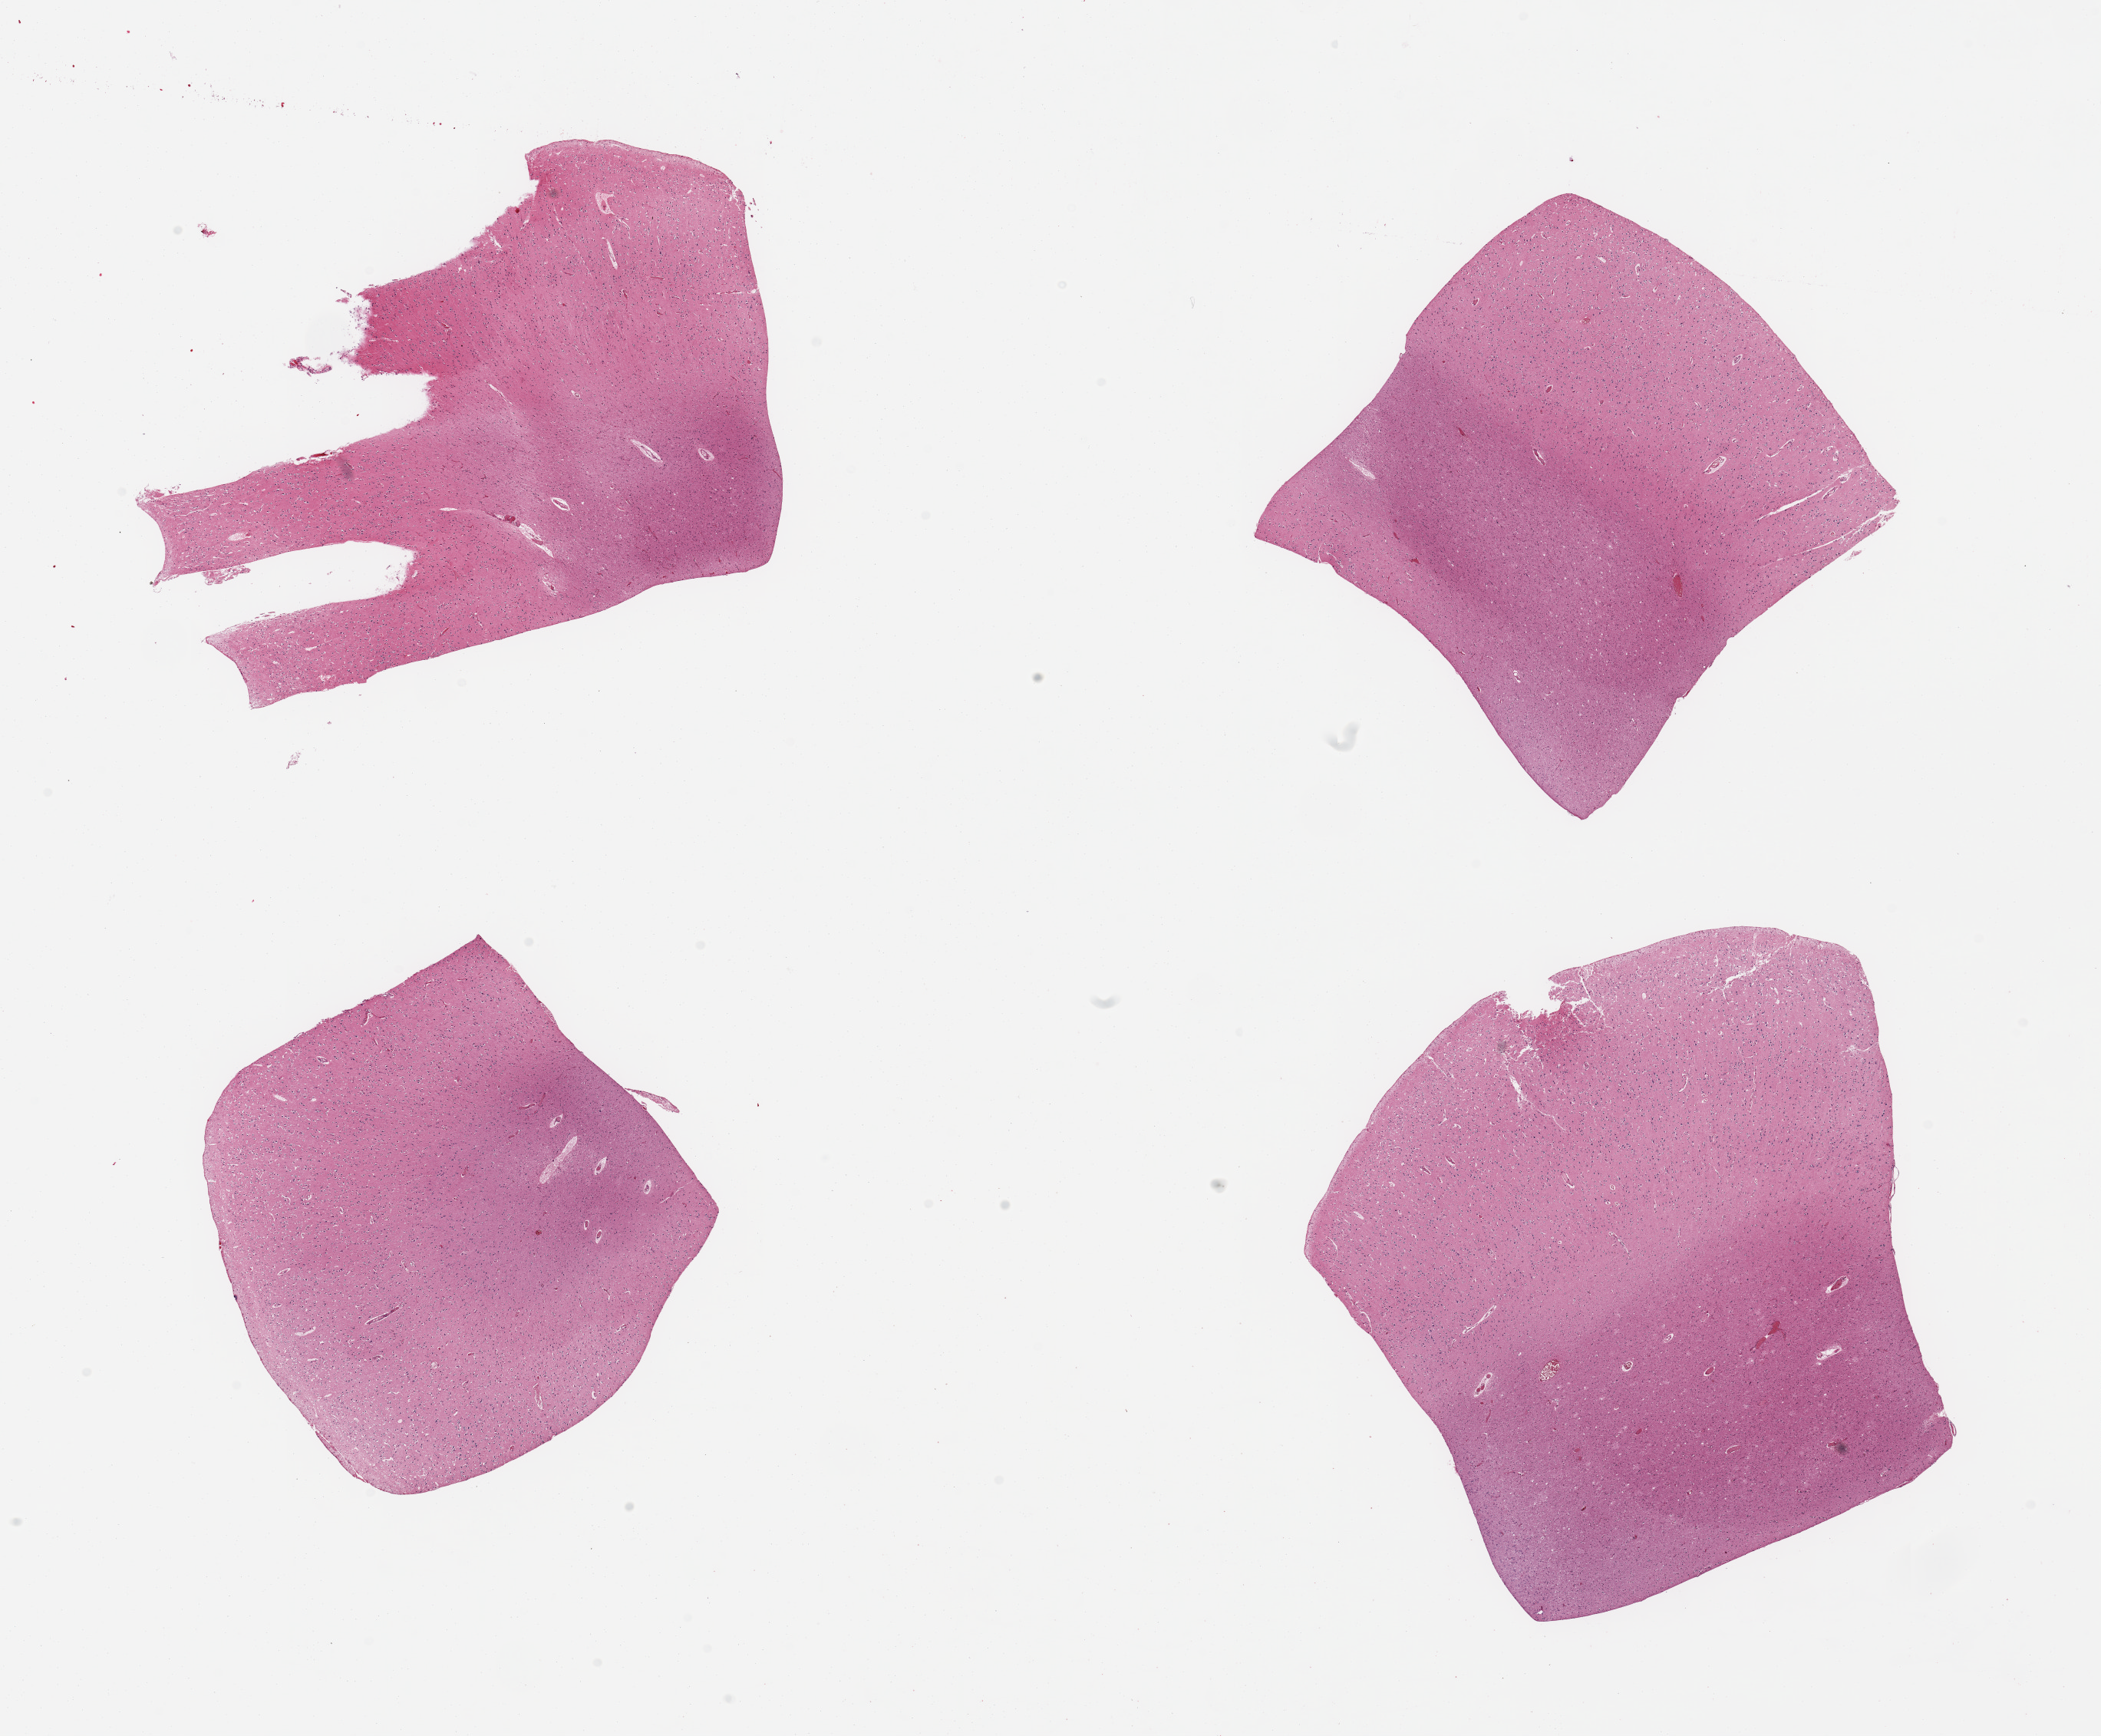
Digitized haematoxylin and eosin-stained section, shown as a low-resolution overview of the whole scanned area (about 21.7 x 17.9 mm, slide scanned at 20x). PAXgene-fixed, paraffin-embedded tissue. Target tissue: cerebral cortex. Tissue donor sample. Donor: male.
Pathologist's review note for this sample: 4 pieces.